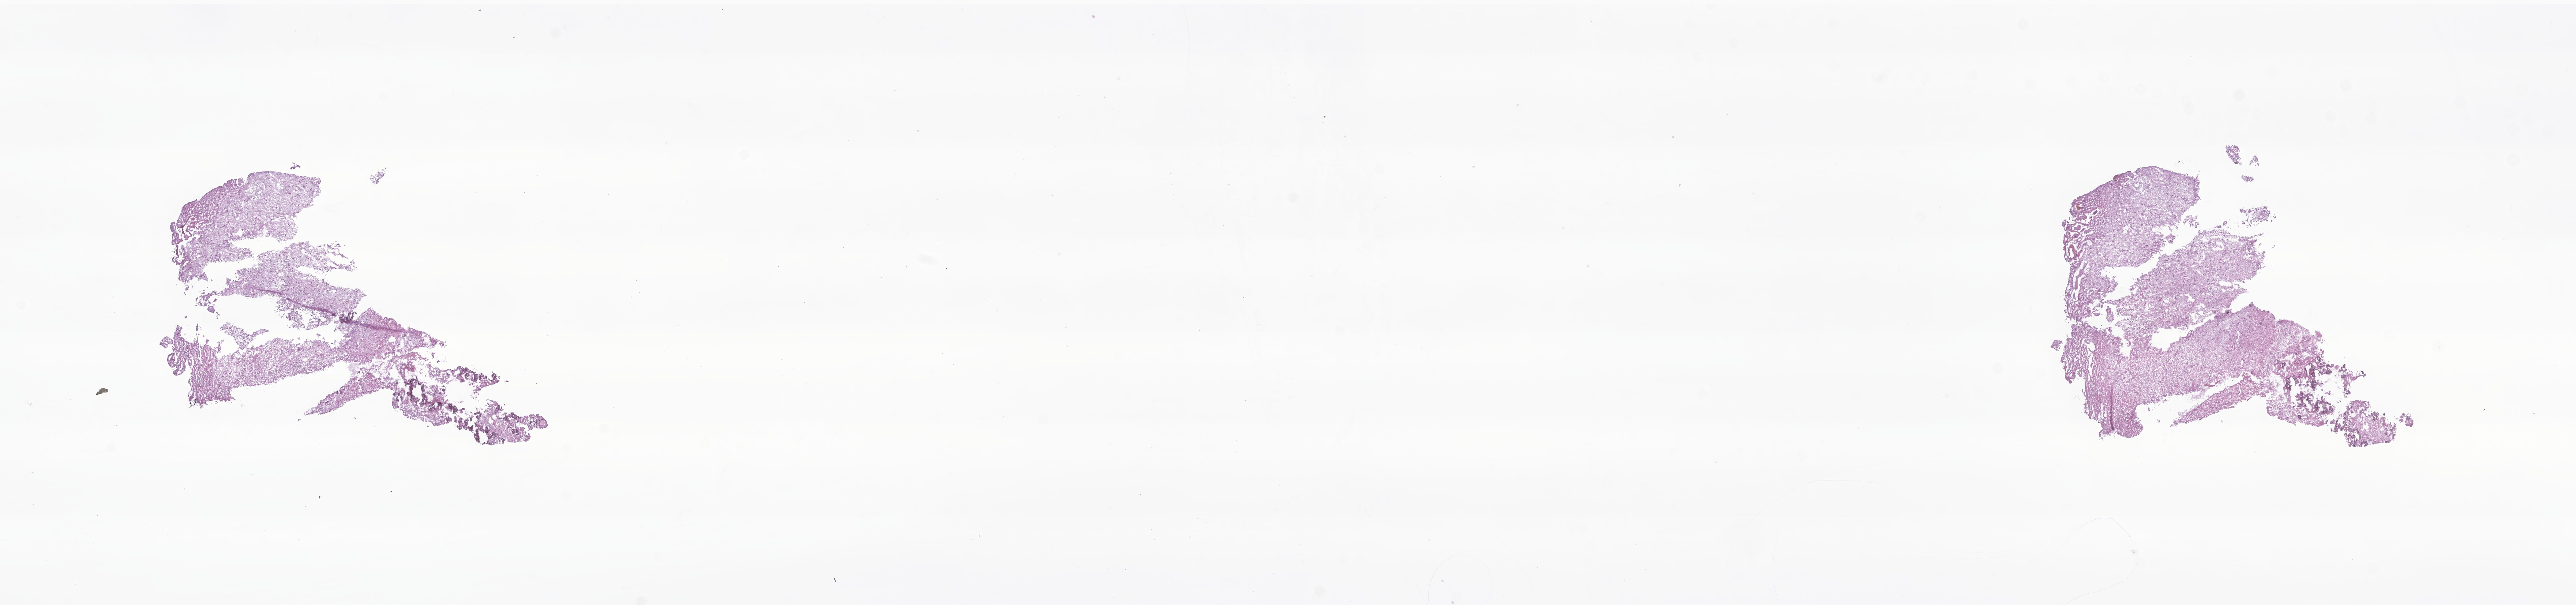
Hematoxylin and eosin (H&E) whole-slide image of tumor tissue from the brain — whole scanned area (about 29.7 x 7.0 mm) shown as a low-resolution overview, frozen section (OCT-embedded). Patient male; age 197 months (16 years 5 months).
Recorded diagnosis: Pilocytic astrocytoma.